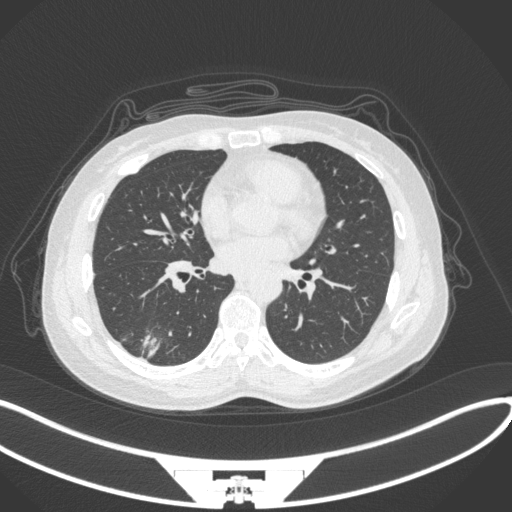
Chest CT, one axial slice; slice 133 of 352 in the series (ordered by position); reconstruction kernel B31f; 120 kVp; lung window (W 1500 / L -600 HU); 1 mm slice thickness; 512 × 512 image matrix, field of view 400 × 400 mm. Female patient, age 55 years. Case-level facts recorded for this patient, not image findings: clinical TNM (as recorded): T1c N1 M0.
Structures marked on this image (rectangle marked by the reading radiologist):
- lung tumour (recorded histology: adenocarcinoma): bounding box (x1, y1, x2, y2) in pixels: (135, 327, 168, 361)